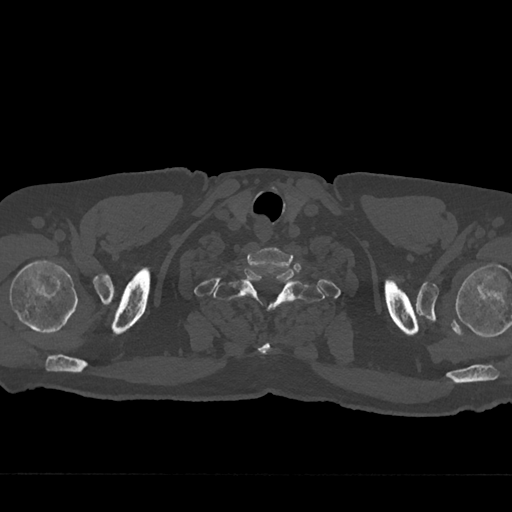
CT including the spine, one axial slice. Slice 669 of 797 in the series (ordered by position). 120 kVp. Bone window (W 1800 / L 400 HU). 0.5 mm slice thickness. 512 × 512 image matrix, field of view 377 × 377 mm. Male patient, age 75 years. Case-level facts recorded for this patient, not image findings: primary cancer: renal.
Outlined on this slice (semi-automatic segmentation, software-assisted and operator-edited):
- T1 vertebra: bounding box <213,269,324,354> (left, top, right, bottom; pixels)